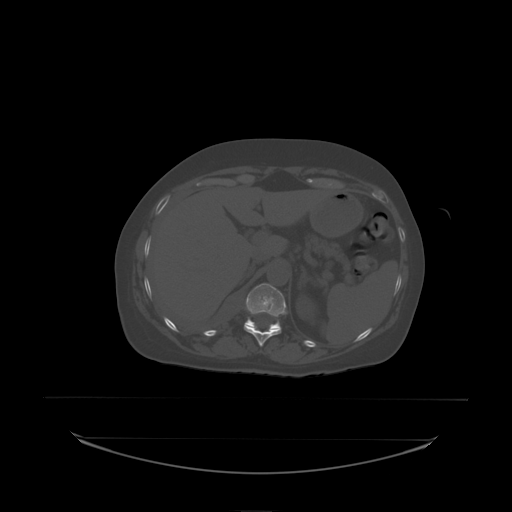
CT including the spine, one axial slice. Position 100 of 242 along the scan axis. Bone window (W 1800 / L 400 HU). 512 × 512 image matrix. Patient: female, 53 years. Case-level facts recorded for this patient, not image findings: primary cancer: lung.
Structures marked on this image (semi-automatically segmented with operator editing):
- T11 vertebra: bounding box <245,325,282,338> (left, top, right, bottom; pixels)
- T12 vertebra: <245,284,287,330>